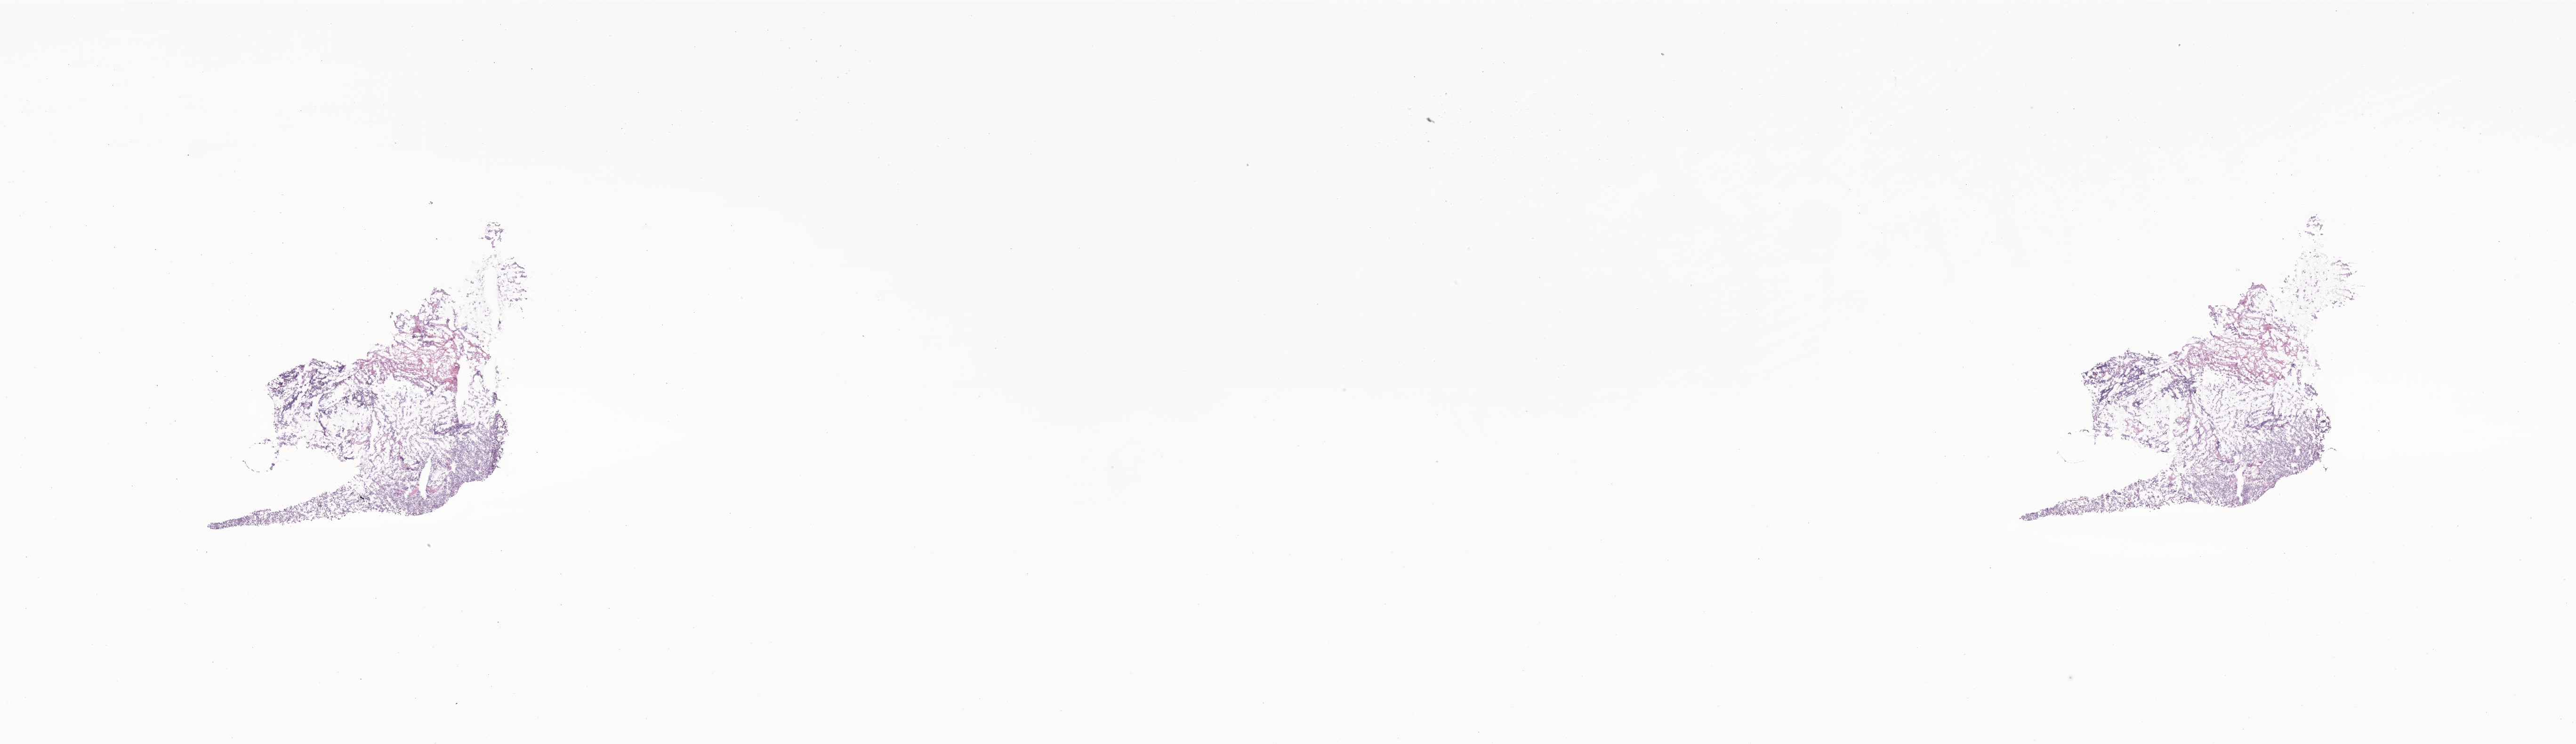
Whole-slide image, hematoxylin and eosin (H&E) stain of tumor tissue from the renal pelvis, low-resolution overview of the scanned area, about 23.1 x 6.7 mm; frozen section. Female patient, age 957 days (about 2.6 years).
Diagnosis (ICD-O-3 morphology term): Neuroblastoma, NOS.